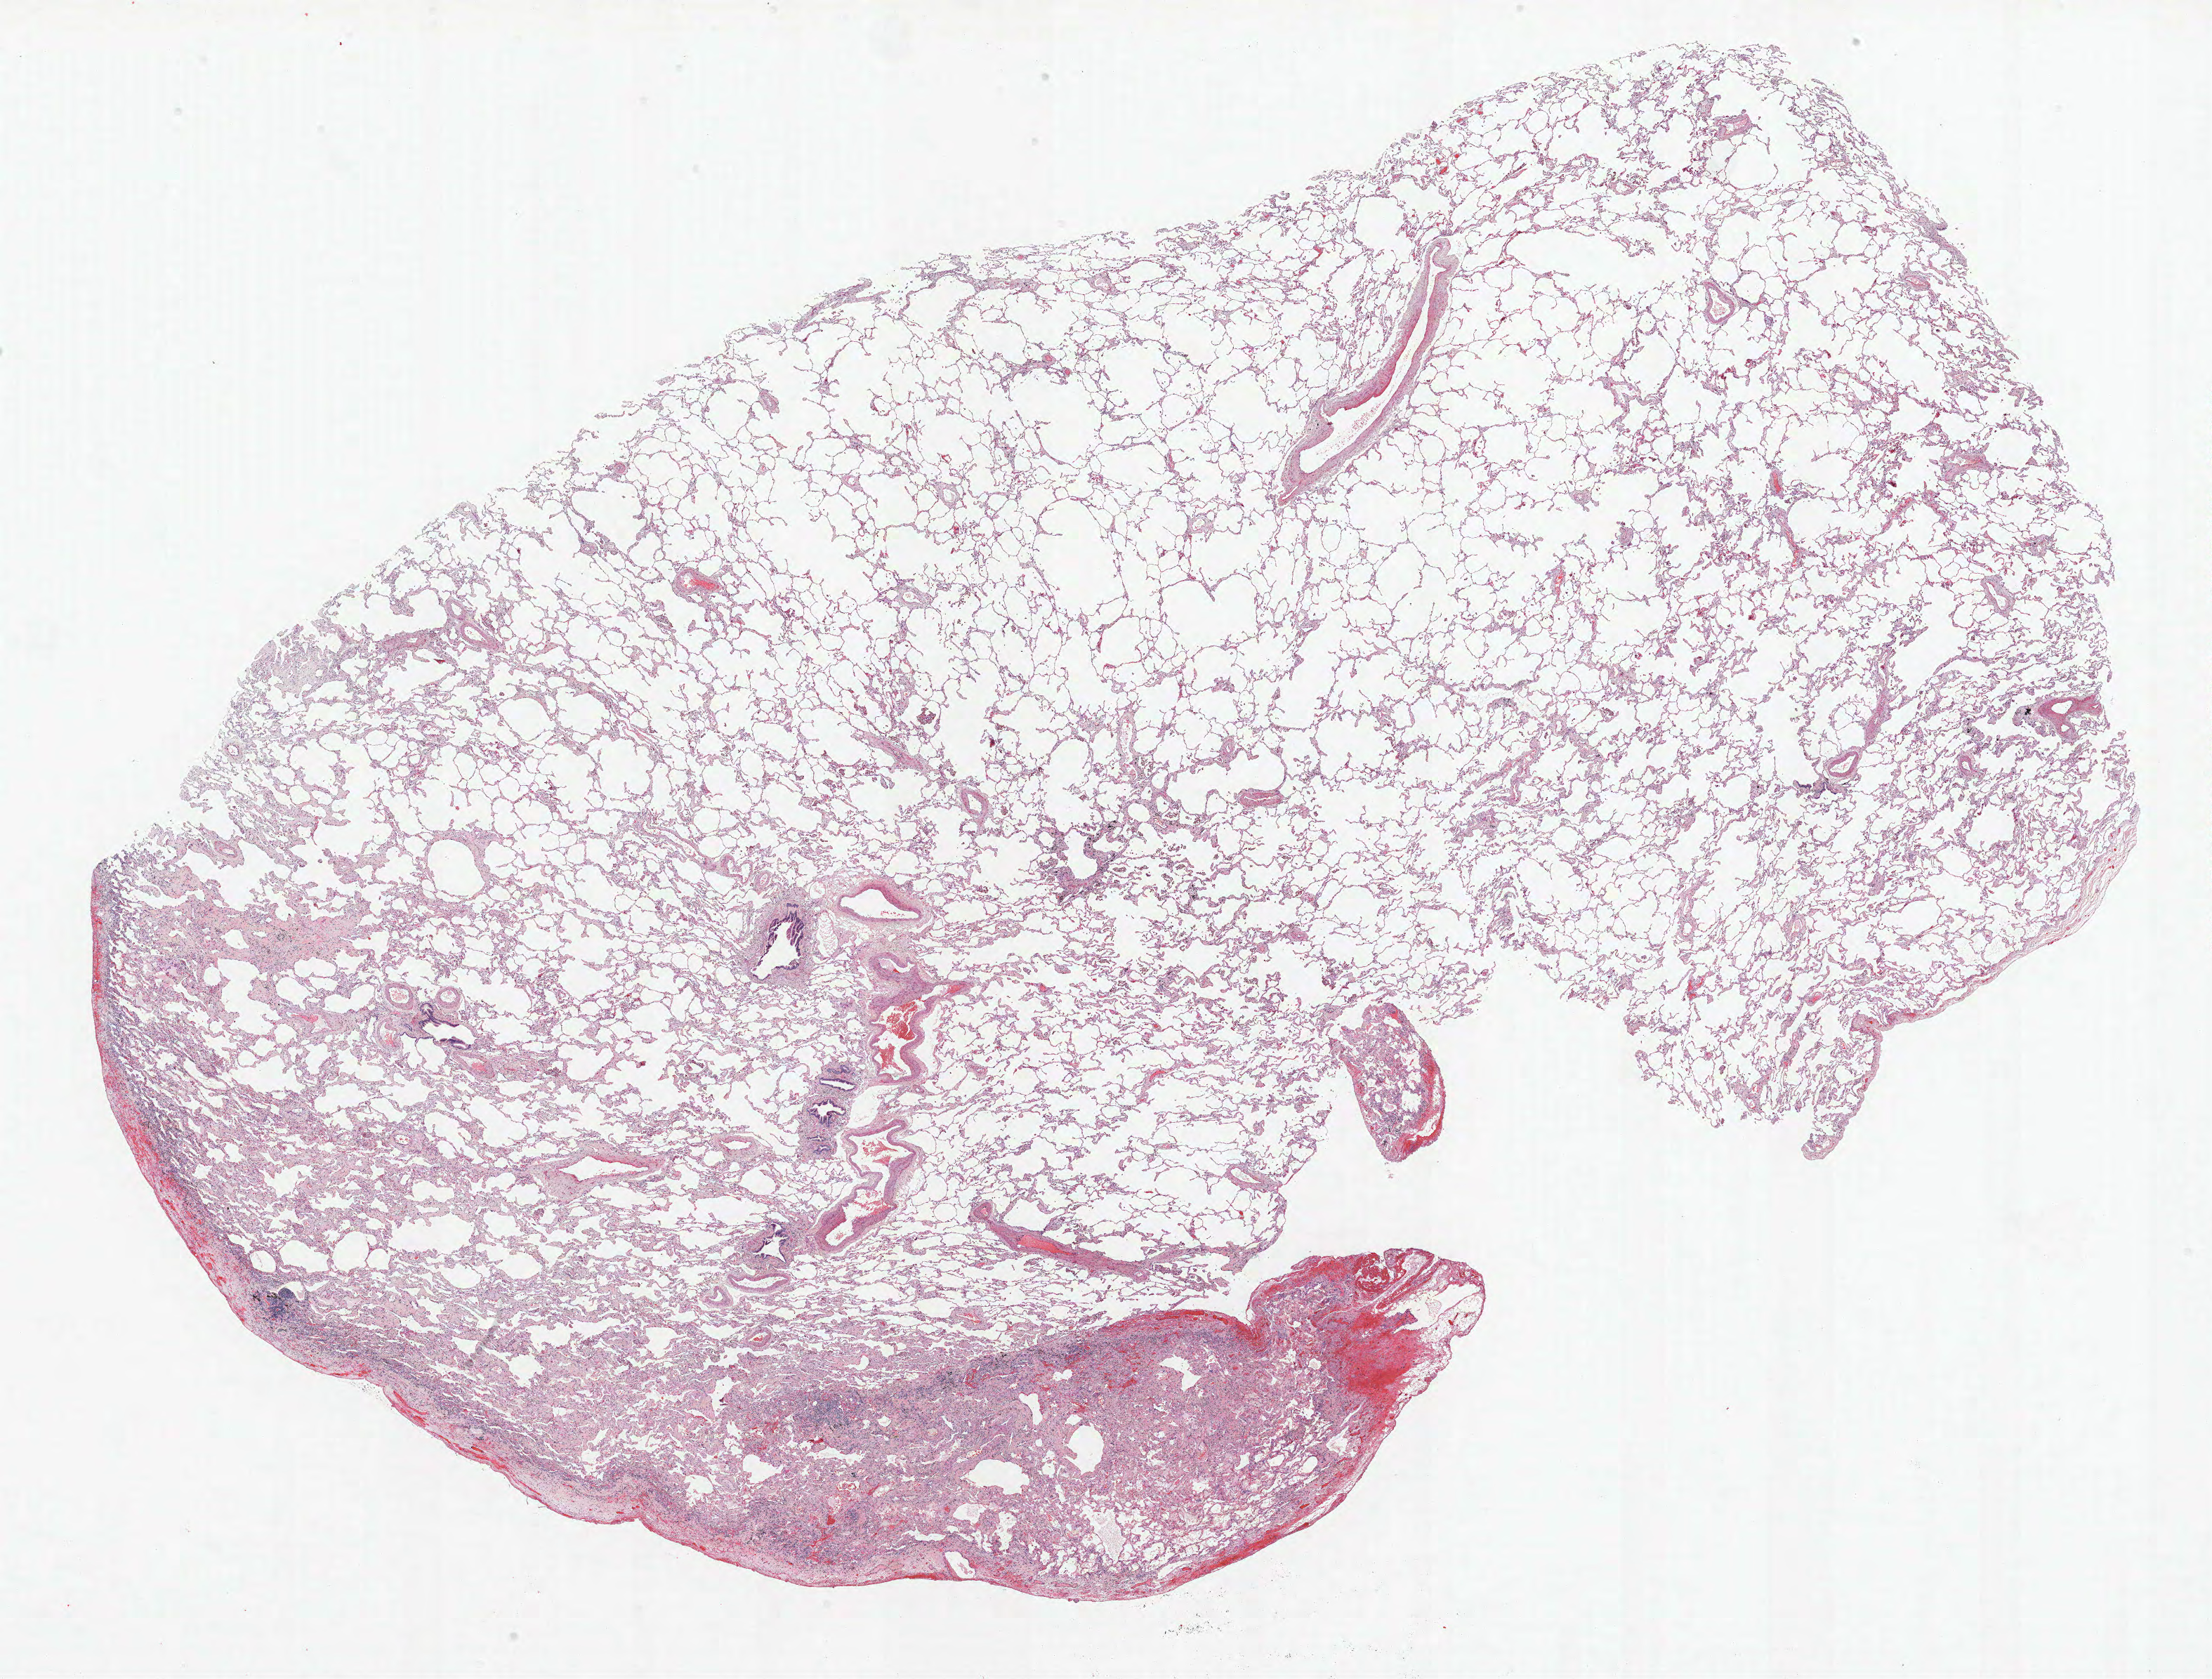
Whole-slide histology image, Hematoxylin and eosin (H&E) stained, low-resolution overview of the scanned area, about 25.2 x 19.1 mm (acquisition: 40x scan), formalin-fixed paraffin-embedded (FFPE) section, lung. Female patient, aged 67 at enrolment. Grade: undifferentiated (G4).
- tumour size (pathology): 135 mm
- participant's lung-cancer diagnosis: Pseudosarcomatous carcinoma
- ICD-O-3 topography: lower lobe of lung (C34.3)
- stage (AJCC 6th edition): IIIB
- primary tumour location (clinical record): right lower lobe